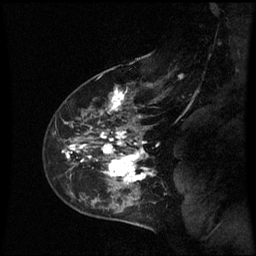
Breast MRI (dynamic contrast-enhanced), one sagittal slice. Slice 43 of 60 in the series (ordered by position). Dynamic contrast-enhanced series, image 2 of 3 at this slice position (ordered by acquisition). 1.5 T. TE 4.2 ms, TR 8.9 ms. 256 × 256 image matrix. Female patient, age 43 years. Case-level facts recorded for this patient, not image findings: setting: breast cancer imaged before/during neoadjuvant chemotherapy; receptor status: HER2-positive.
Annotated regions visible in this slice (semi-automatic segmentation, software-assisted and operator-edited):
- analysis volume of interest (the breast-tissue region the enhancement analysis was run in; not a lesion): bounding box <56,80,160,195> (left, top, right, bottom; pixels)
- tumour enhancement mask (voxels above the 70 % enhancement threshold inside the analysis volume of interest): <62,88,152,185>